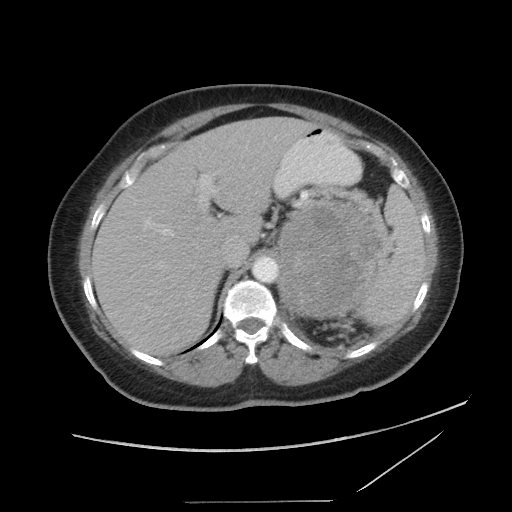
Contrast-enhanced abdominal CT, one axial slice. 120 kVp. Intravenous contrast given. Soft-tissue window (W 400 / L 40 HU). 5 mm slice thickness. 512 × 512 image matrix, field of view 398 × 398 mm. Patient: female, 77 years. From the clinical record (not read from this slice): diagnosis: adrenocortical carcinoma; tumour side: left adrenal; tumour size at pathology: 13.1 cm; Ki-67 index: 10 %; stage (as recorded): 3.
Outlined on this slice (semi-automatically segmented with operator editing):
- mass: bounding box <279,200,378,314> (left, top, right, bottom; pixels)